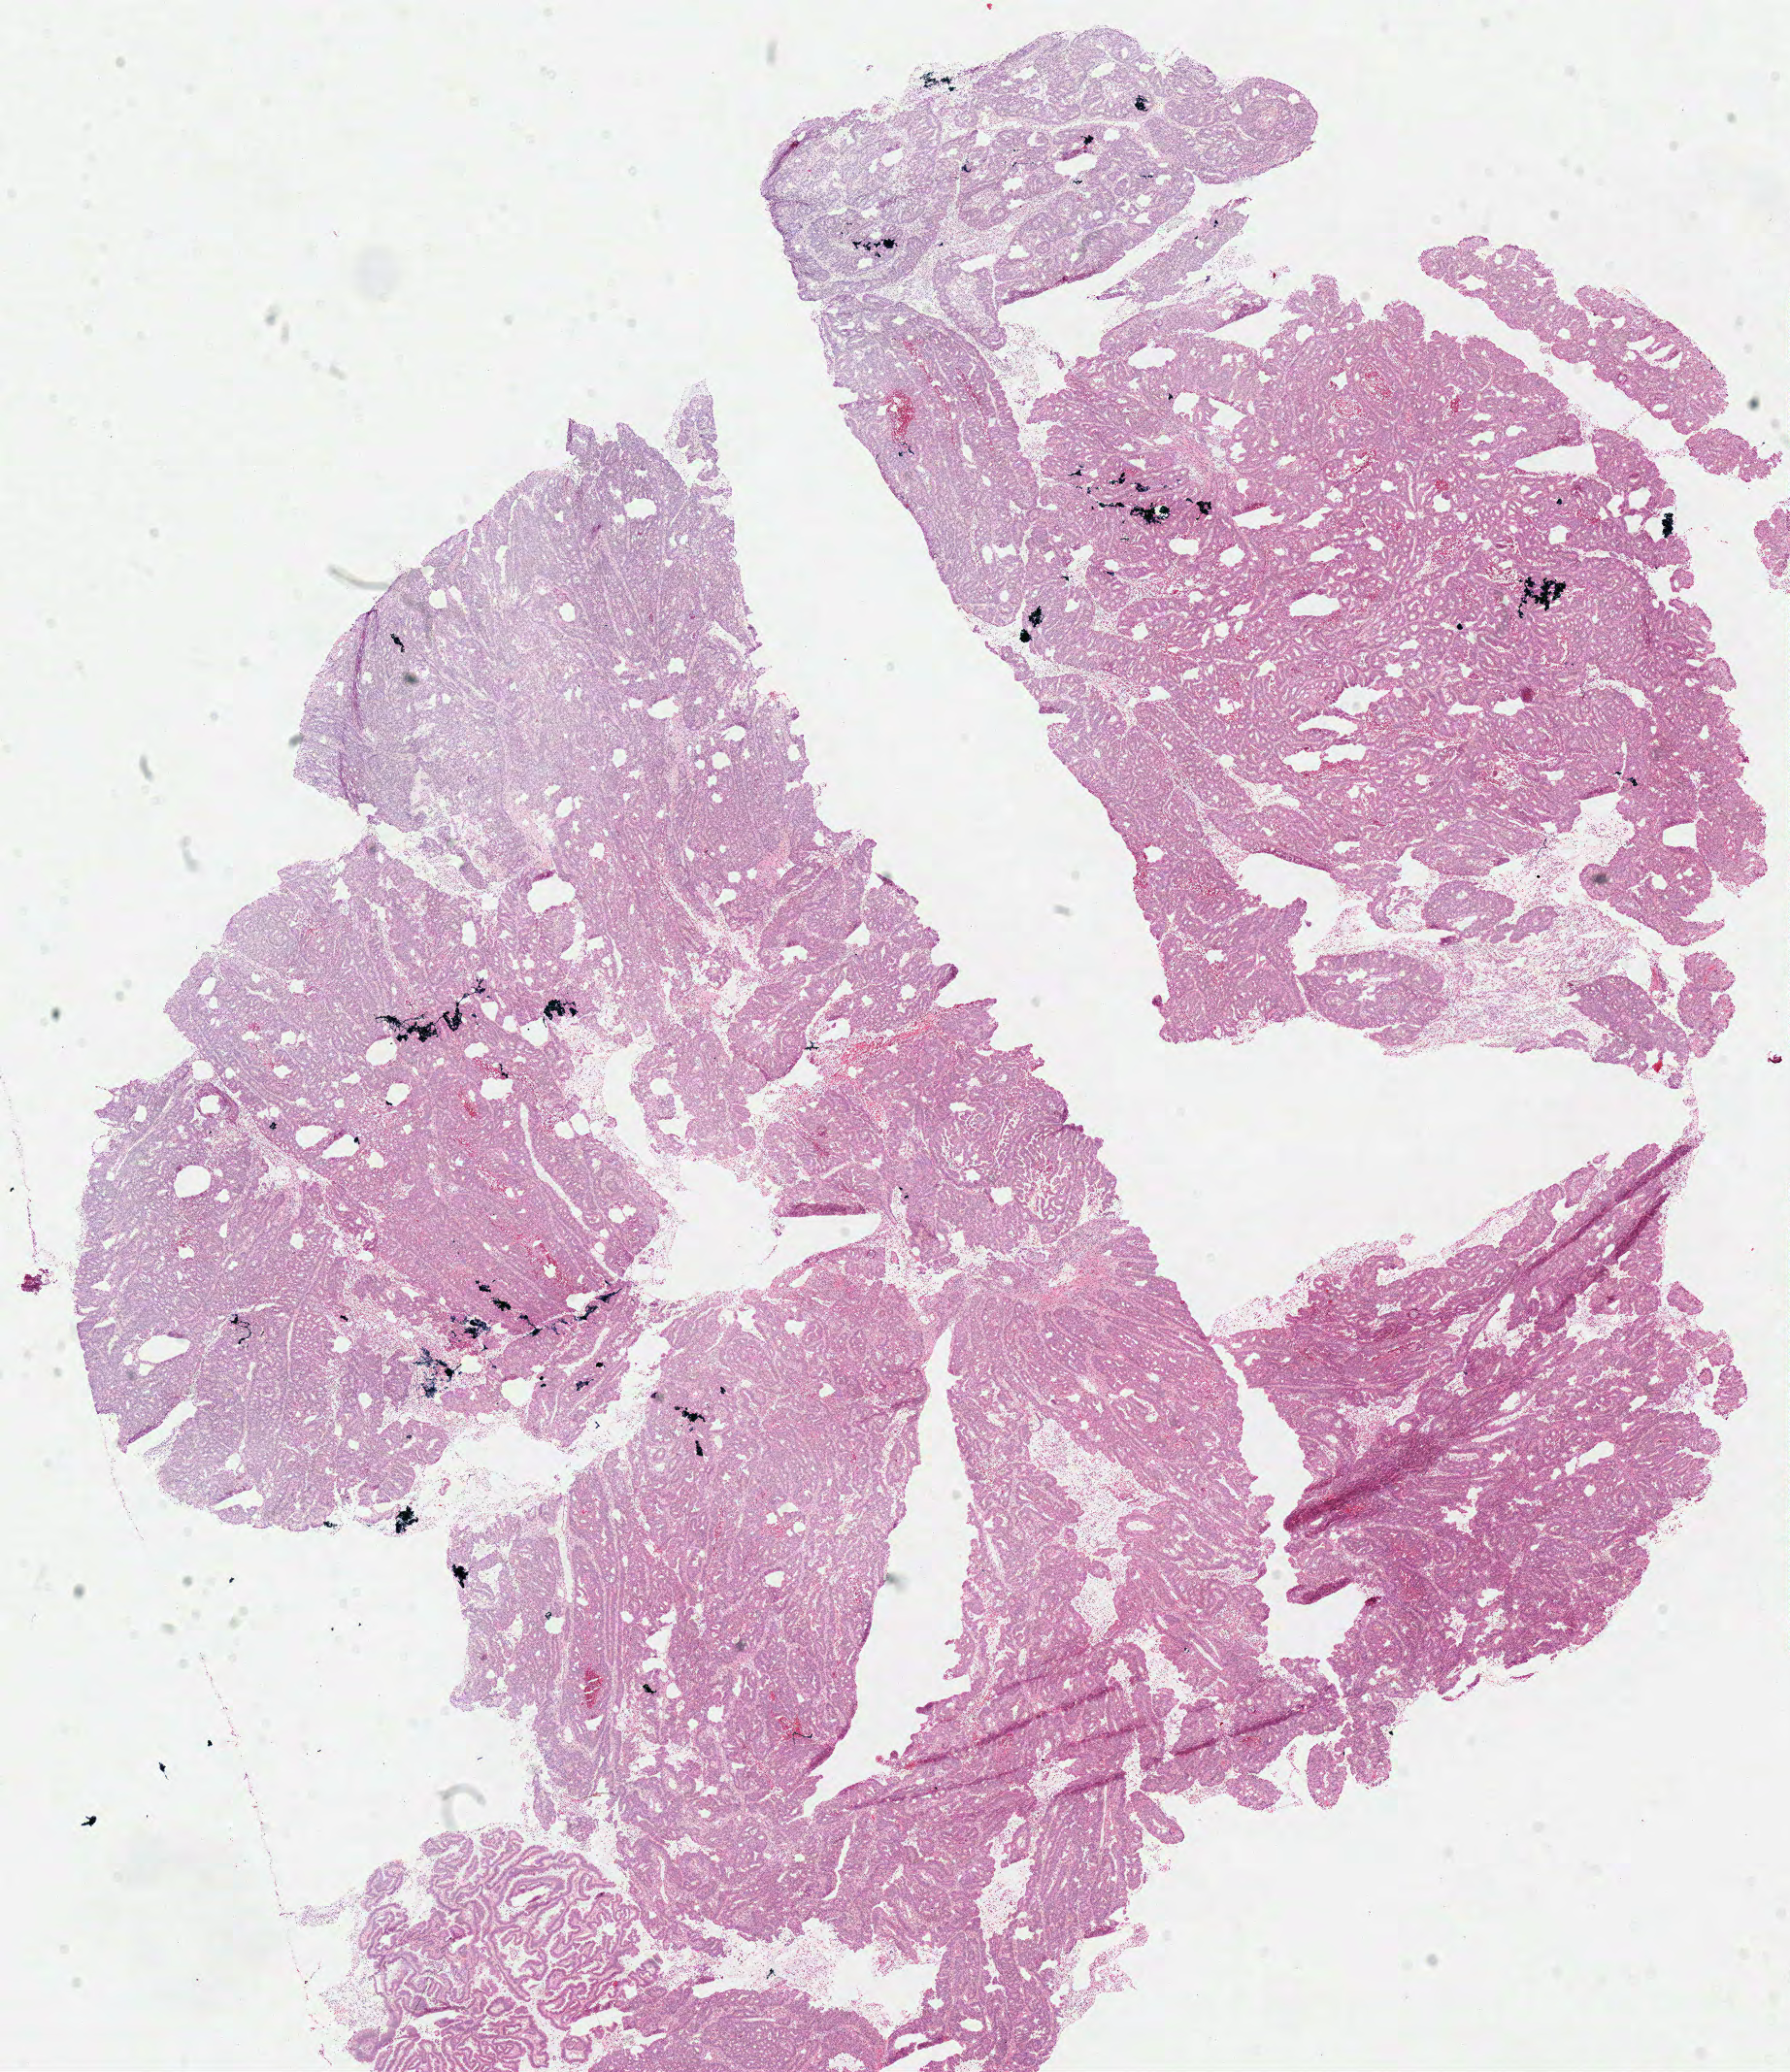
Digitized Hematoxylin and eosin (H&E) stained tissue section (whole slide), whole scanned area (about 14.5 x 16.8 mm, slide scanned at 40x) shown as a low-resolution overview, frozen section from the top of the tissue portion, primary tumour sample from the colon. Patient: female, age at initial diagnosis 77 years. Composition of this section per pathologist review: tumour cells 79%, tumour nuclei 85%, normal cells 5%, stromal cells 8%, necrosis 8%.
Histologic diagnosis: Adenocarcinoma, NOS. AJCC pathologic stage: I.